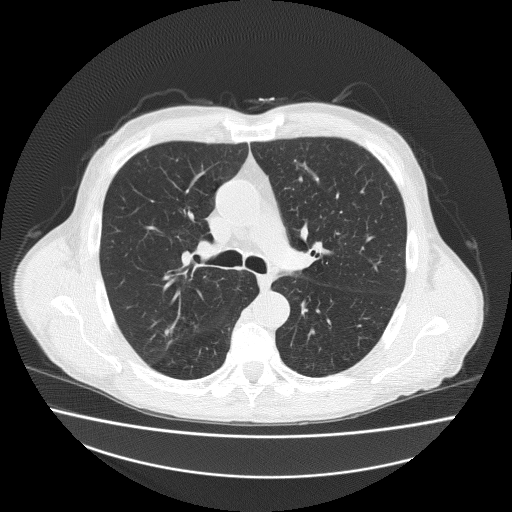
Chest CT (low-dose screening protocol), one axial image, second screening round (one year after baseline), lung window (W 1500 / L -600 HU), 2 mm slice thickness, slice 76 of 186 in the series. Male participant, aged 73 years at enrolment. Current smoker at enrolment.
Expert reader's lesion annotation, bounding box (x1, y1, x2, y2) in pixels: (152, 309, 206, 347). Screening reader's record for this exam: no non-calcified nodule ≥4 mm recorded. Lung cancer was diagnosed 418 days after this screen: adenosquamous carcinoma, right upper lobe, well differentiated (G1), stage IA (AJCC 6th edition), 20 mm at pathology.